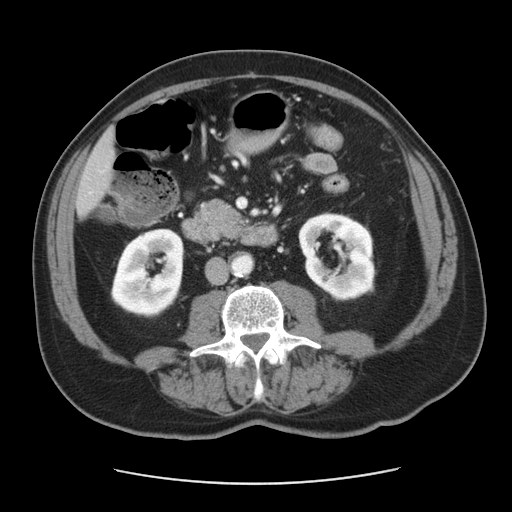
Contrast-enhanced abdominal CT, one axial slice. Position 12 of 42 along the scan axis. 120 kVp. Soft-tissue window (W 400 / L 40 HU). 5 mm slice thickness. 512 × 512 image matrix, field of view 370 × 370 mm. Male patient, age 73 years. Case-level facts recorded for this patient, not image findings: diagnosis: colorectal cancer liver metastases, imaged before liver resection; multiple liver metastases: yes; largest metastasis: 0.5 cm.
Annotated regions visible in this slice (expert manual segmentation):
- liver: bounding box <77,134,113,214> (left, top, right, bottom; pixels)